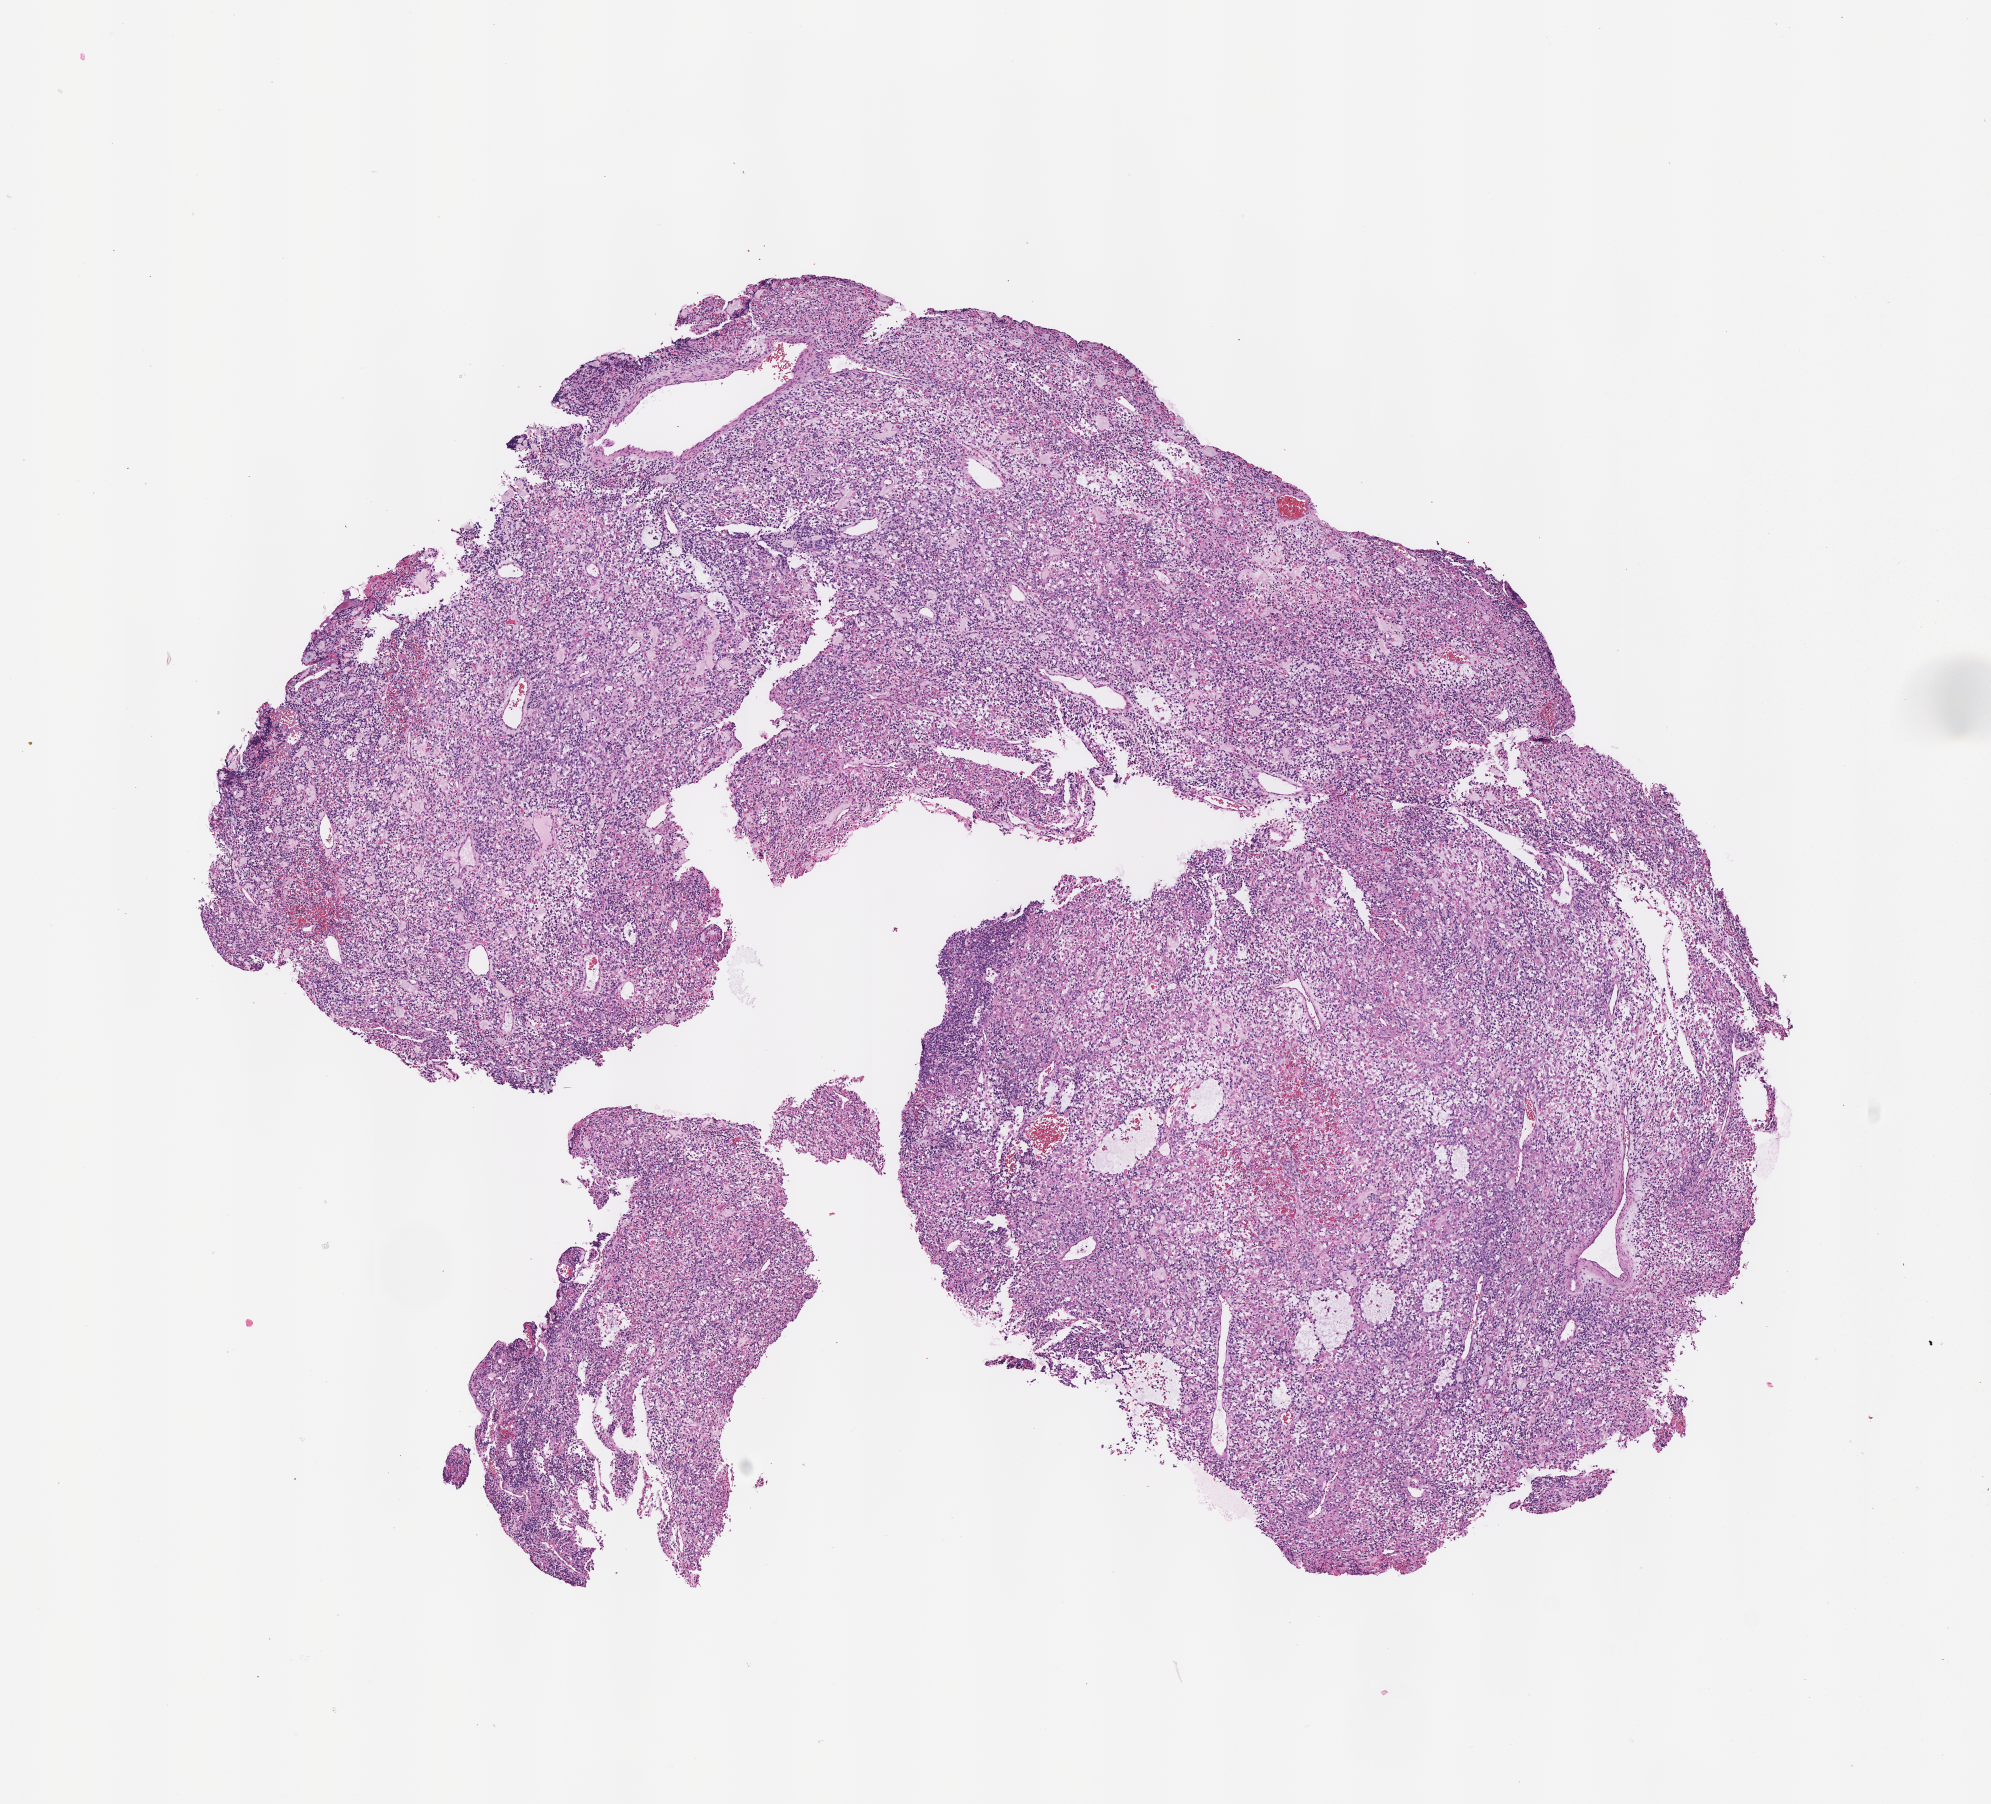
Digitized haematoxylin and eosin-stained section of tumor tissue — a low-resolution overview of the entire scanned area, about 8.1 x 7.3 mm, formalin-fixed paraffin-embedded section, site: retropharynx, right. Male patient, age at diagnosis 13.2 years.
Diagnosis: rhabdomyosarcoma; histological classification: embryonal rhabdomyosarcoma.